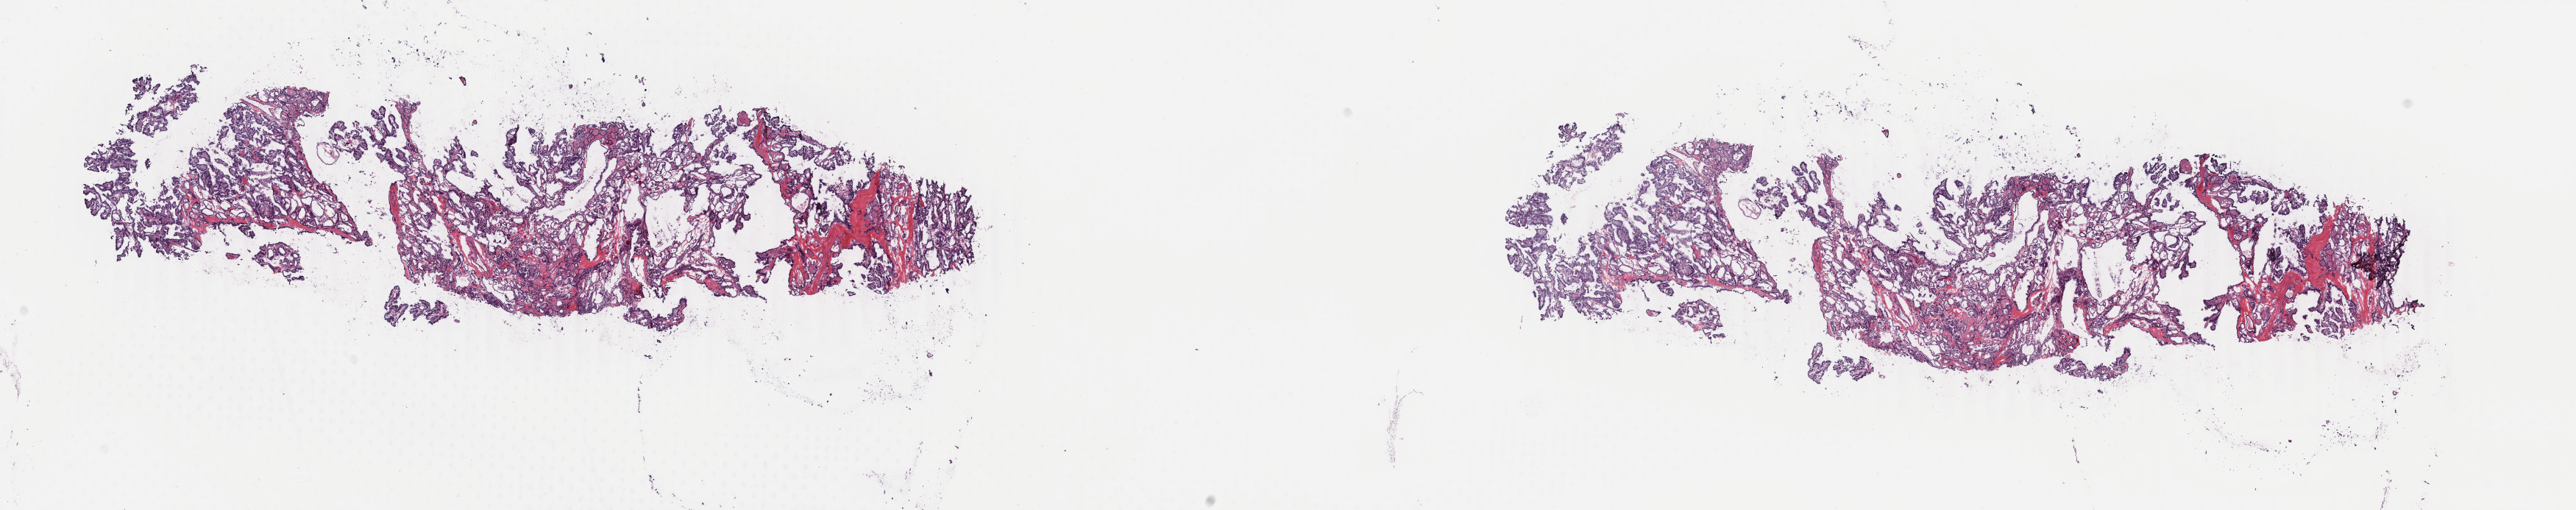
Whole-slide histology image, H&E-stained — shown as a low-resolution overview of the whole scanned area (about 27.8 x 5.5 mm, acquisition: 40x scan), frozen section from the top of the tissue portion, sample: primary tumour, thyroid. Female patient; age at initial diagnosis 61 years. Pathologist review of this section (percent, as recorded): tumour cells 85%, tumour nuclei 85%, normal cells 0%, stromal cells 15%, necrosis 0%. Inflammatory infiltration, as recorded: lymphocyte infiltration 1%, monocyte infiltration 1%, neutrophil infiltration 0%.
• pathologic diagnosis: Papillary adenocarcinoma, NOS
• lymph nodes positive (case pathology): 0 of 4 examined
• AJCC pathologic stage: I (7th edition)